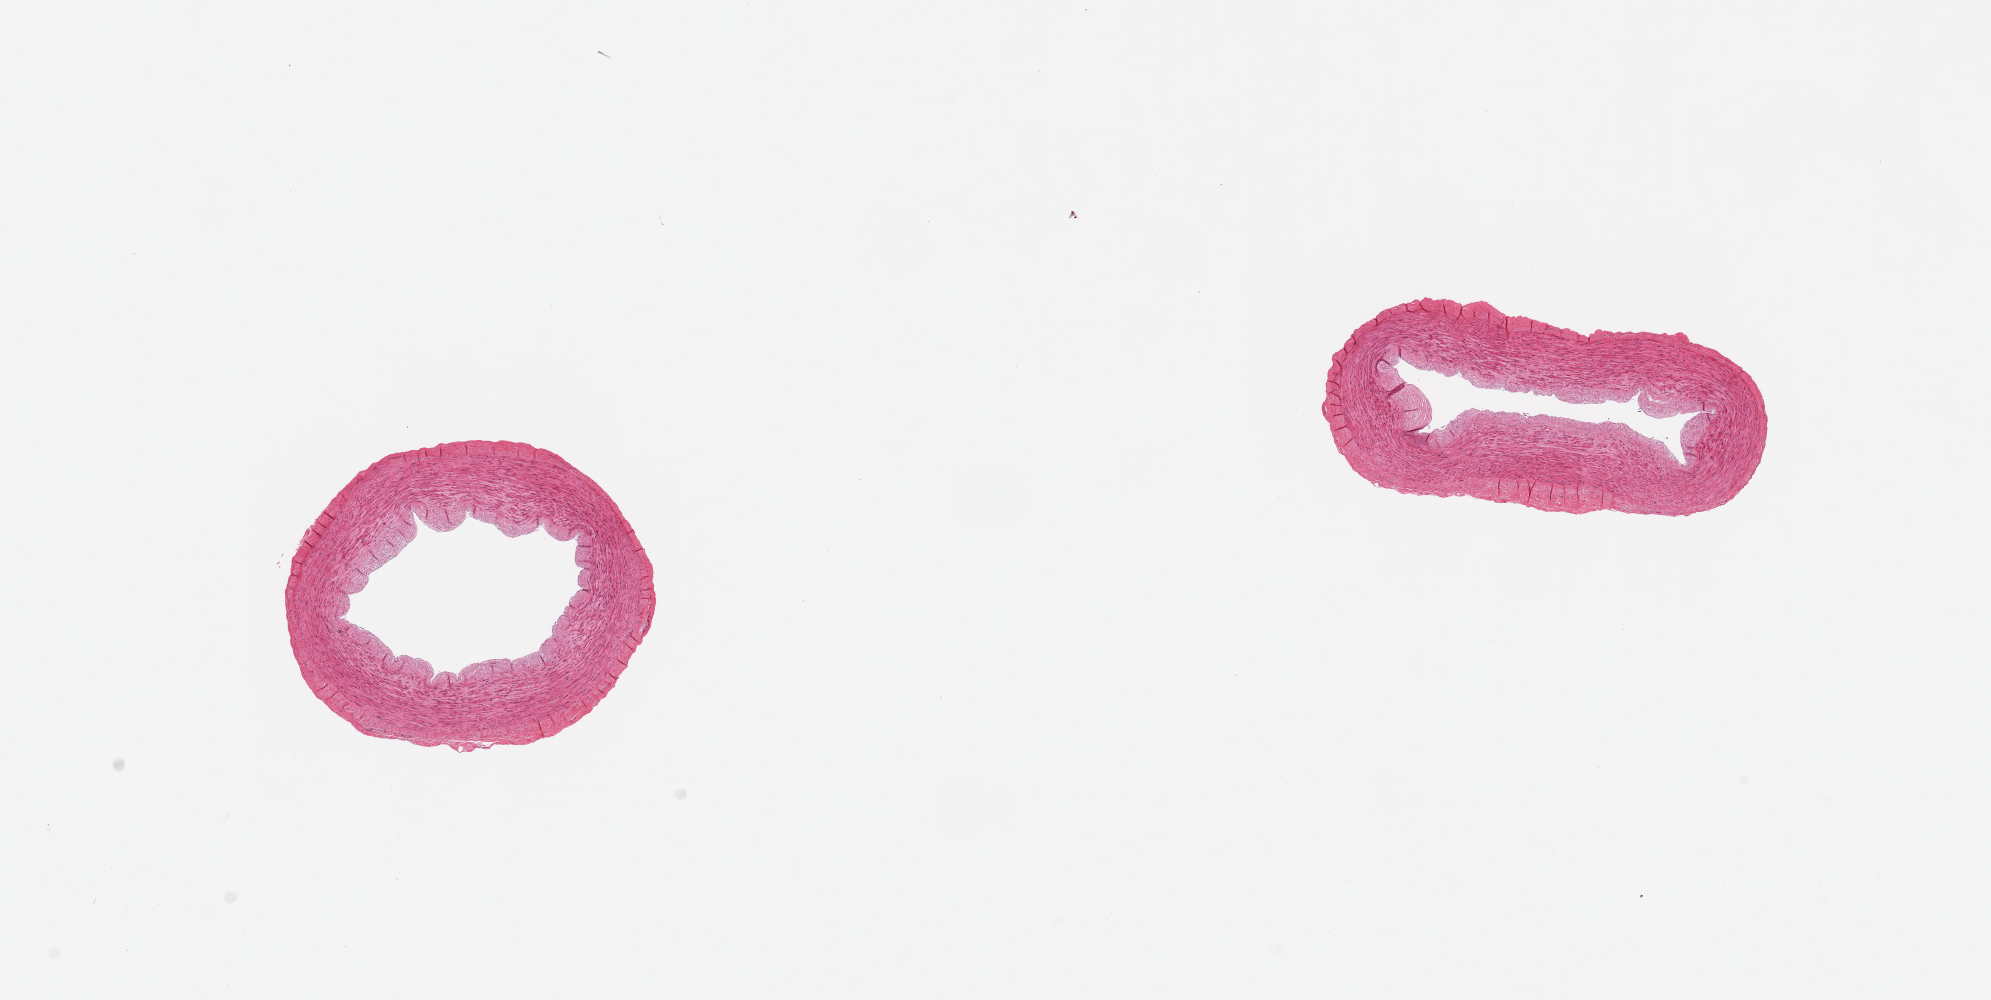
Whole-slide image, haematoxylin and eosin stain, low-resolution overview of the scanned area, about 15.8 x 7.9 mm. PAXgene-fixed paraffin-embedded (PFPE) section. Section of tibial artery (target tissue). Donor tissue sample. Donor: male.
* review note (as recorded): 2 pieces, no significant atherosis or adherent fat